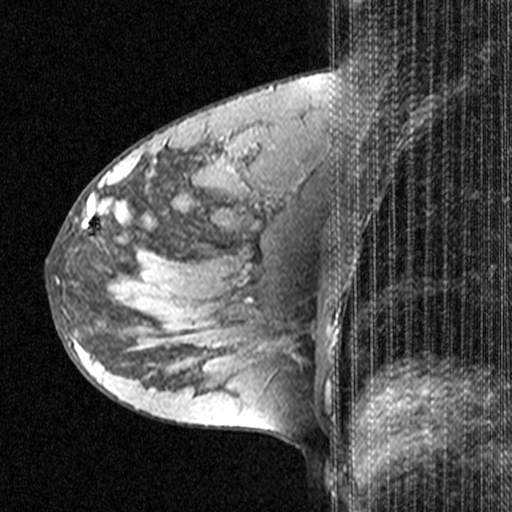
Breast MRI (dynamic contrast-enhanced), one sagittal slice. Slice 21 of 44 in the series (ordered by position). Dynamic contrast-enhanced study with each time point stored as its own series, time point 2 of 3 at this slice position (early post-contrast, ordered by acquisition time). 1.5 T. TE 4.5 ms, TR 11 ms. 3 mm slice thickness. 512 × 512 image matrix. Patient: female, 28 years. From the clinical record (not read from this slice): setting: breast cancer imaged before/during neoadjuvant chemotherapy; receptor status: HR-positive, HER2-negative.
Annotated regions visible in this slice (semi-automatically segmented with operator editing):
- analysis volume of interest (the breast-tissue region the enhancement analysis was run in; not a lesion): bounding box <48,182,151,283> (left, top, right, bottom; pixels)
- tumour enhancement mask (voxels above the 90 % enhancement threshold inside the analysis volume of interest): <84,182,102,226>